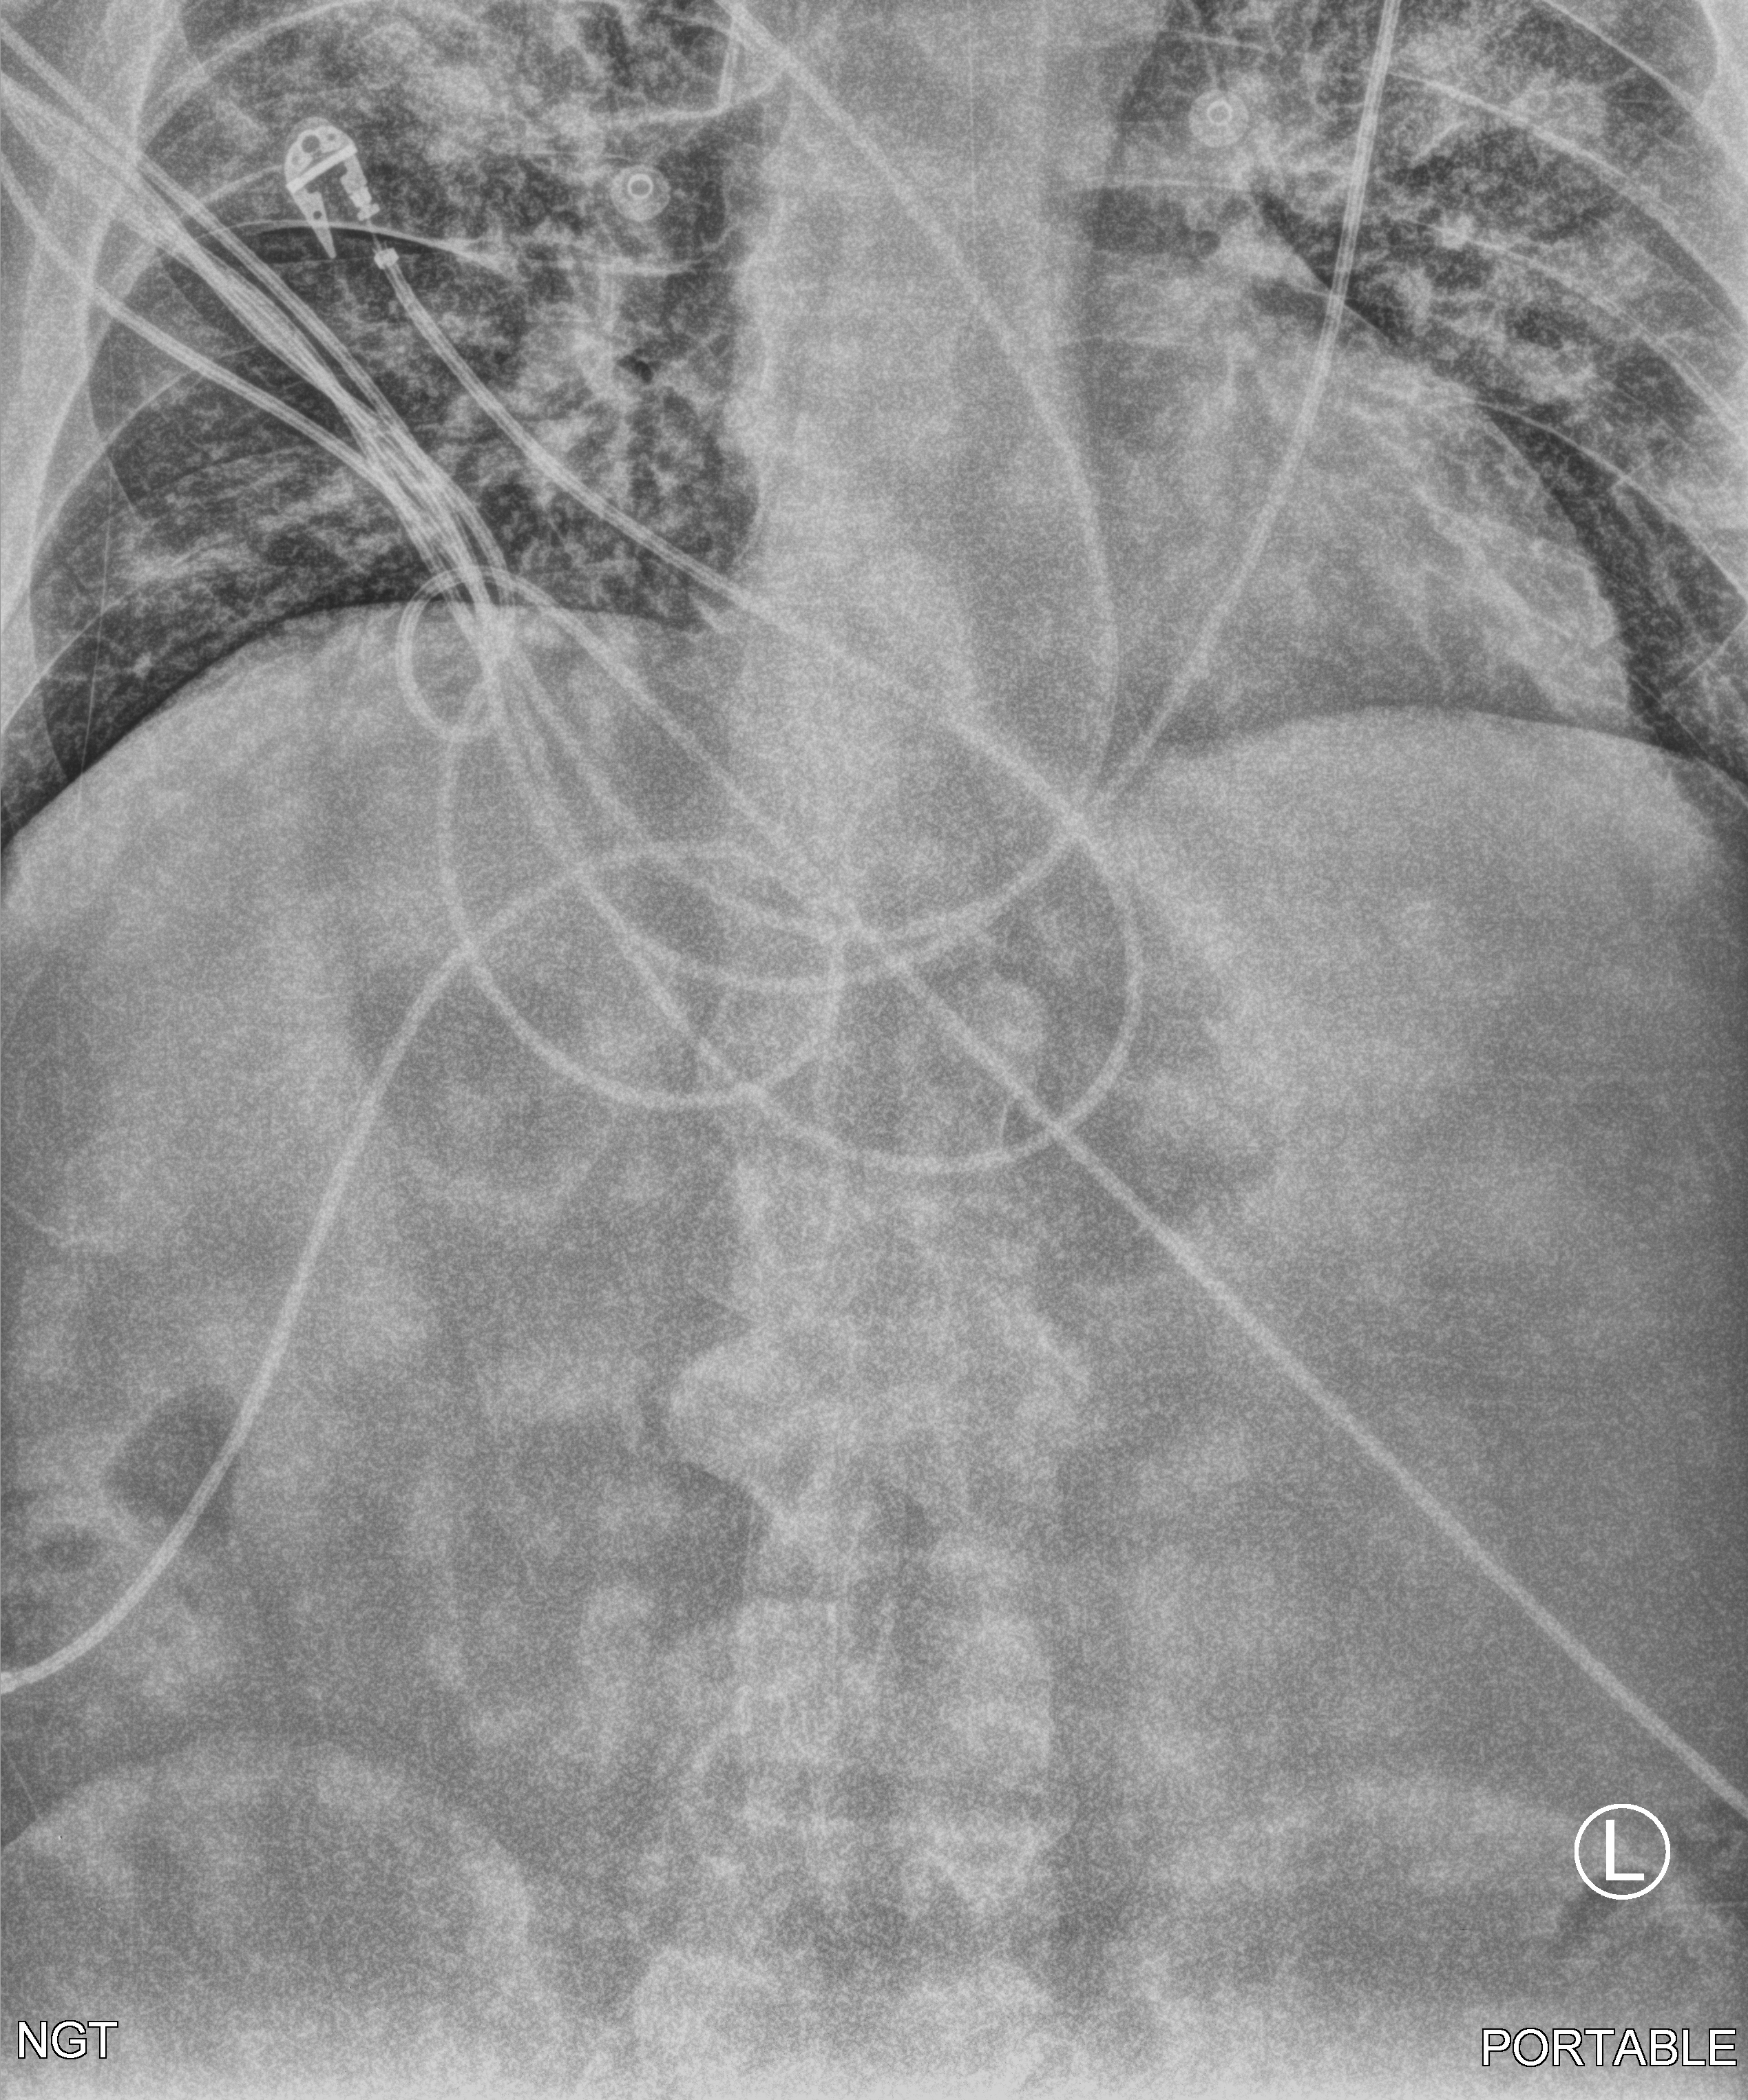
Portable chest radiograph, anteroposterior (AP) projection. Male patient hospitalised with COVID-19, age 75–90 years.
From the hospital-stay record, not from the radiograph (when in the stay this image was taken is not recorded):
- chronic kidney disease (admission record): no
- hypertension (admission record): no
- admitted to intensive care during this hospital stay: yes